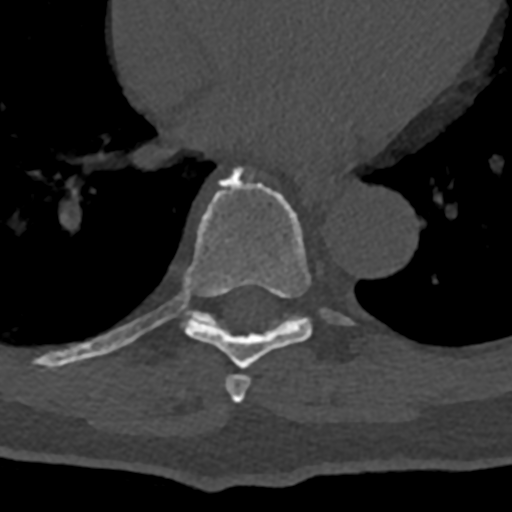
CT including the spine, one axial slice. Slice 701 of 797 in the series (ordered by position). Reconstruction kernel Br40s/3. Bone window (W 1800 / L 400 HU). 0.5 mm slice thickness. 512 × 512 image matrix, field of view 160 × 160 mm. Patient: male, 74 years. Case-level facts recorded for this patient, not image findings: primary cancer: renal; vertebrae with lytic lesions (as recorded): T10, L1, L2, L3, L4, L5.
Annotated regions visible in this slice (semi-automatic segmentation, software-assisted and operator-edited):
- T7 vertebra: bounding box (x1, y1, x2, y2) in pixels: (225, 374, 251, 403)
- T8 vertebra: (70, 166, 355, 369)
- T9 vertebra: (181, 294, 311, 327)